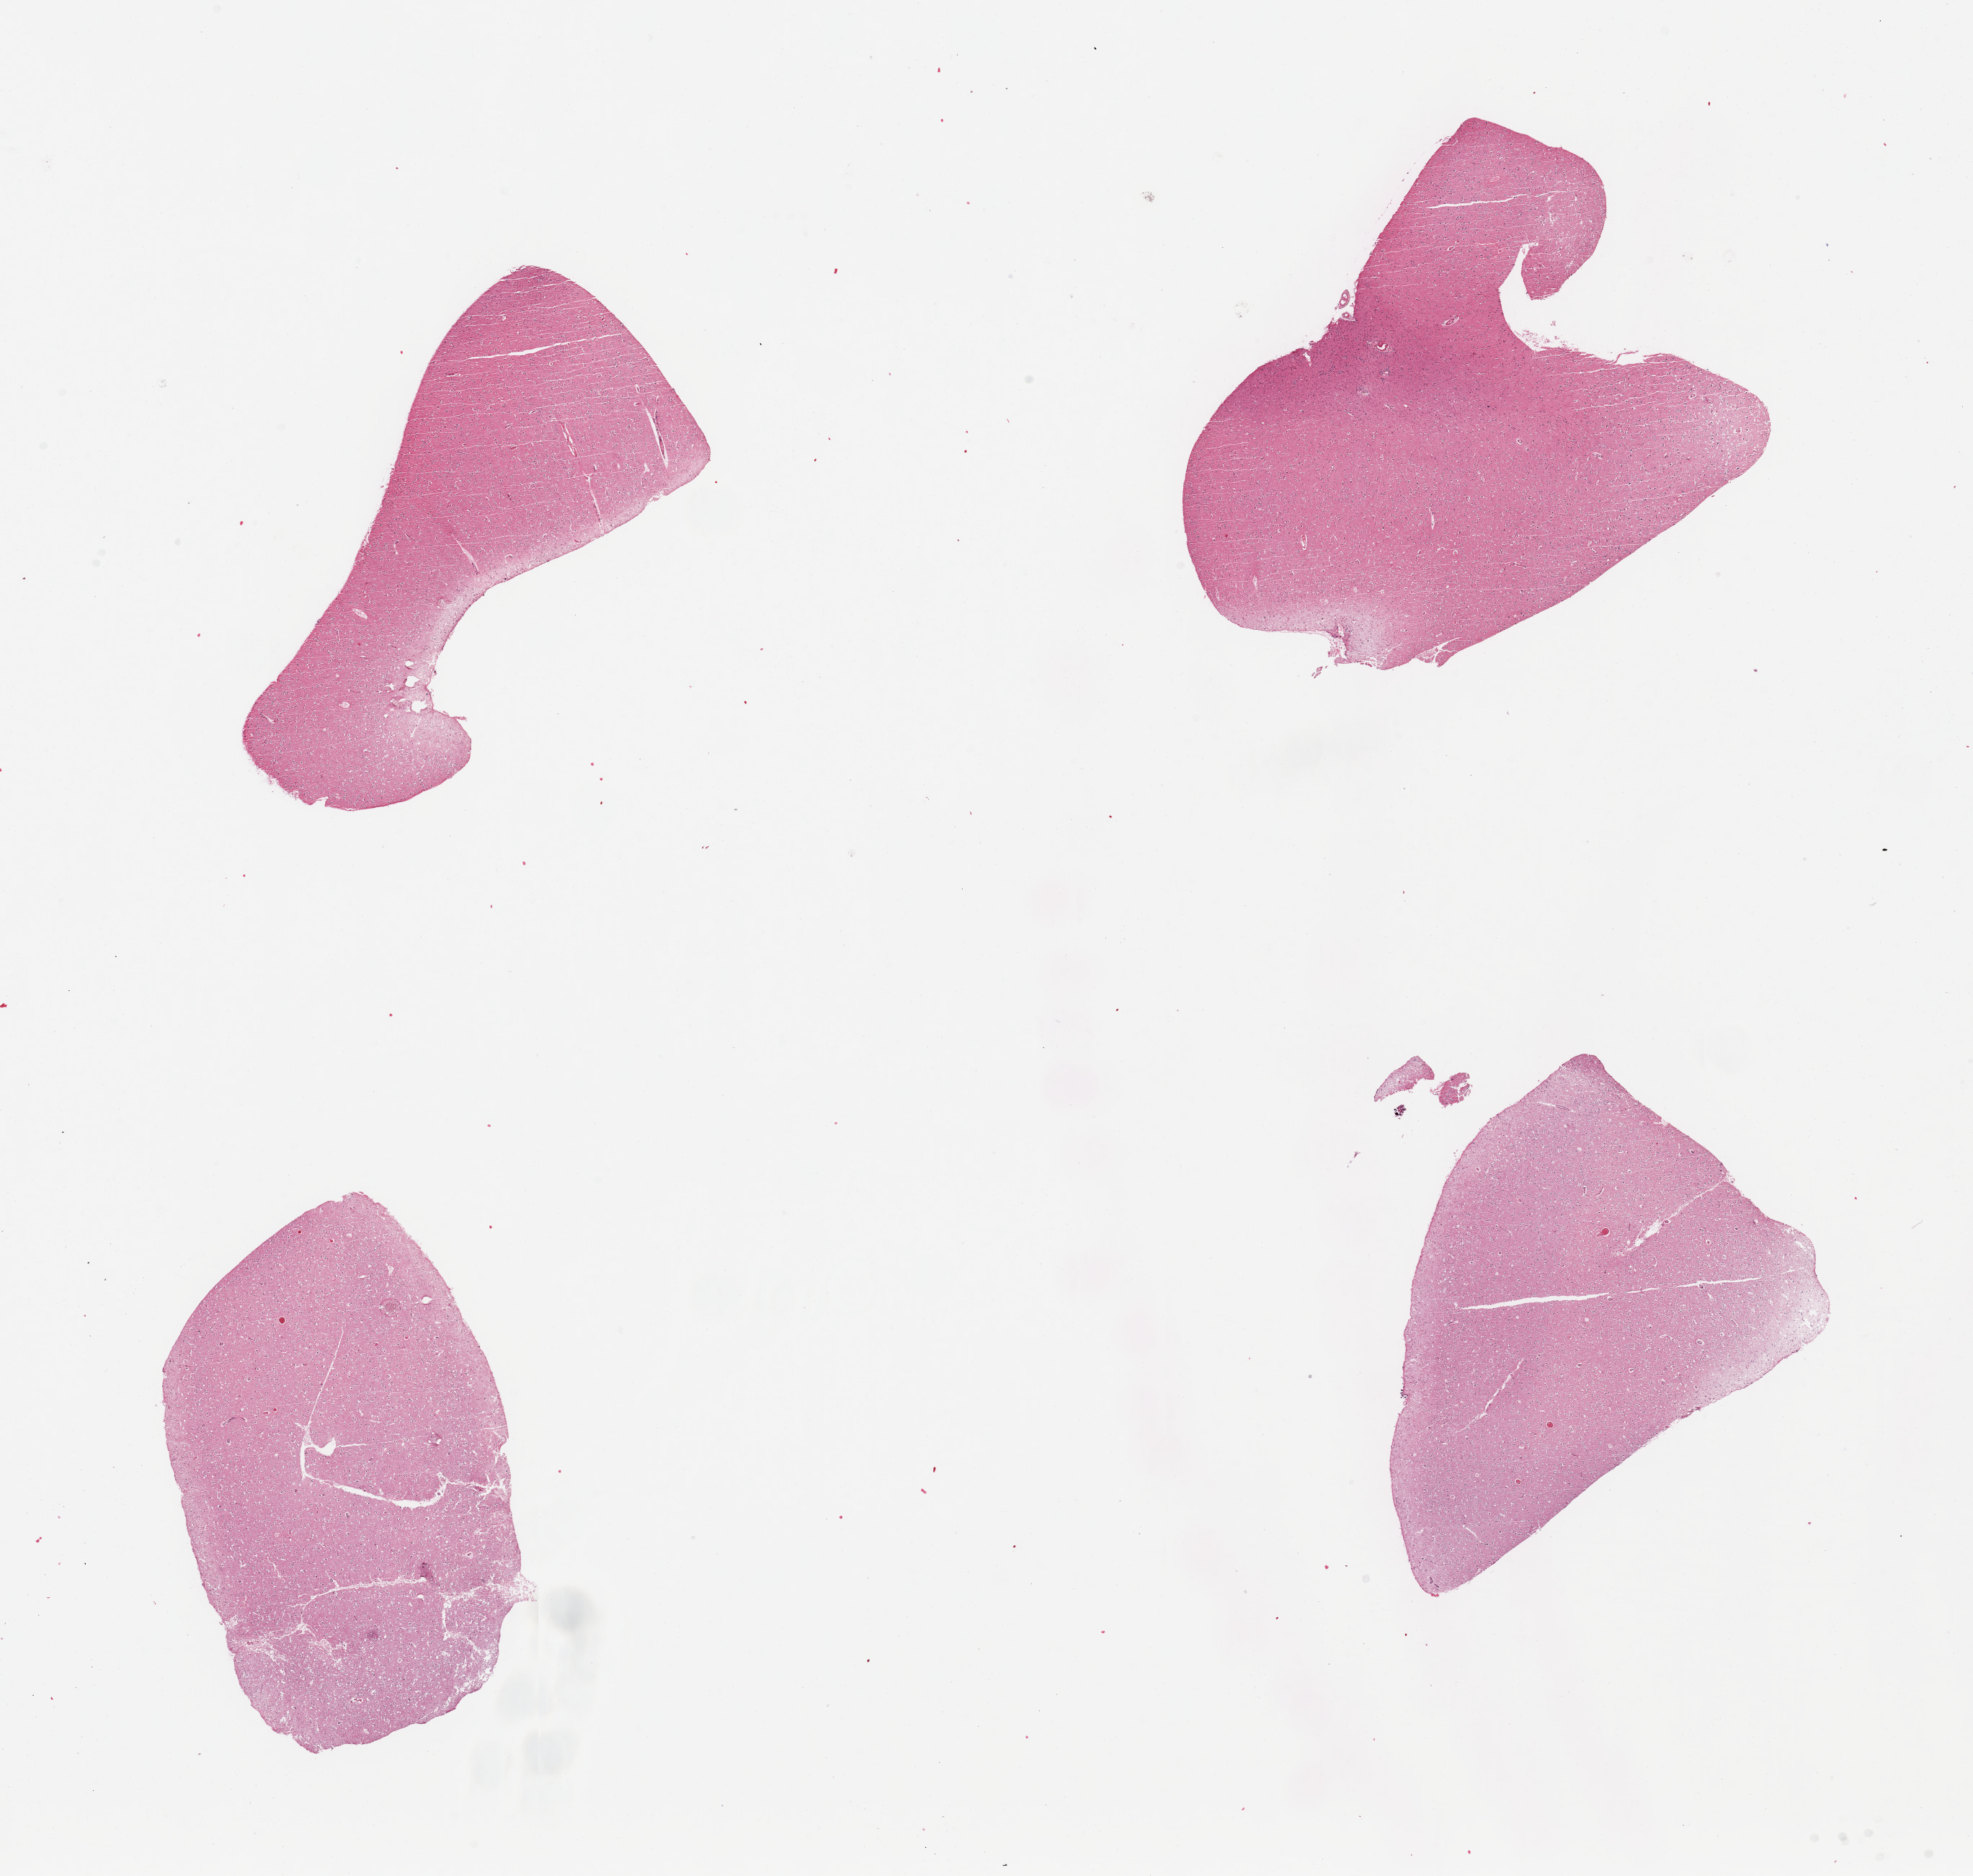
Digitized hematoxylin and eosin (H&E)-stained section, brightfield — a low-resolution overview of the entire scanned area, about 21.7 x 20.6 mm (acquisition: 20x scan); PAXgene-fixed, paraffin-embedded tissue; target tissue: cerebral cortex; donor tissue sample. Donor sex: male.
Pathologist's review note for this sample: 4 pieces.